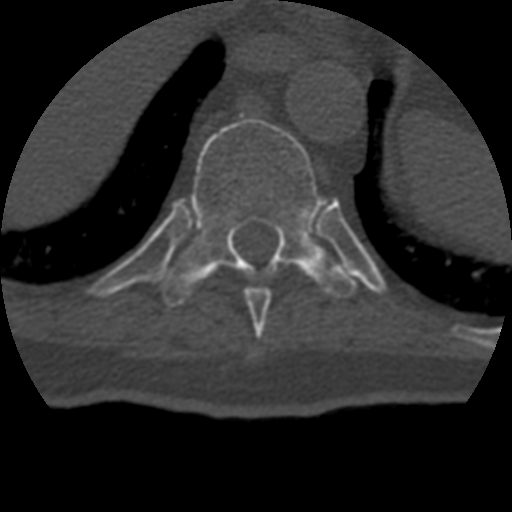
CT including the spine, one axial slice. Slice 226 of 399 in the series (ordered by position). Reconstruction kernel STANDARD. Bone window (W 1800 / L 400 HU). 1.25 mm slice thickness. 512 × 512 image matrix, field of view 160 × 160 mm. Patient age 69 years. From the clinical record (not read from this slice): primary cancer: prostate.
Annotated regions visible in this slice (semi-automatic segmentation, software-assisted and operator-edited):
- T10 vertebra: bounding box (x1, y1, x2, y2) in pixels: (162, 118, 357, 307)
- T9 vertebra: (244, 287, 271, 329)